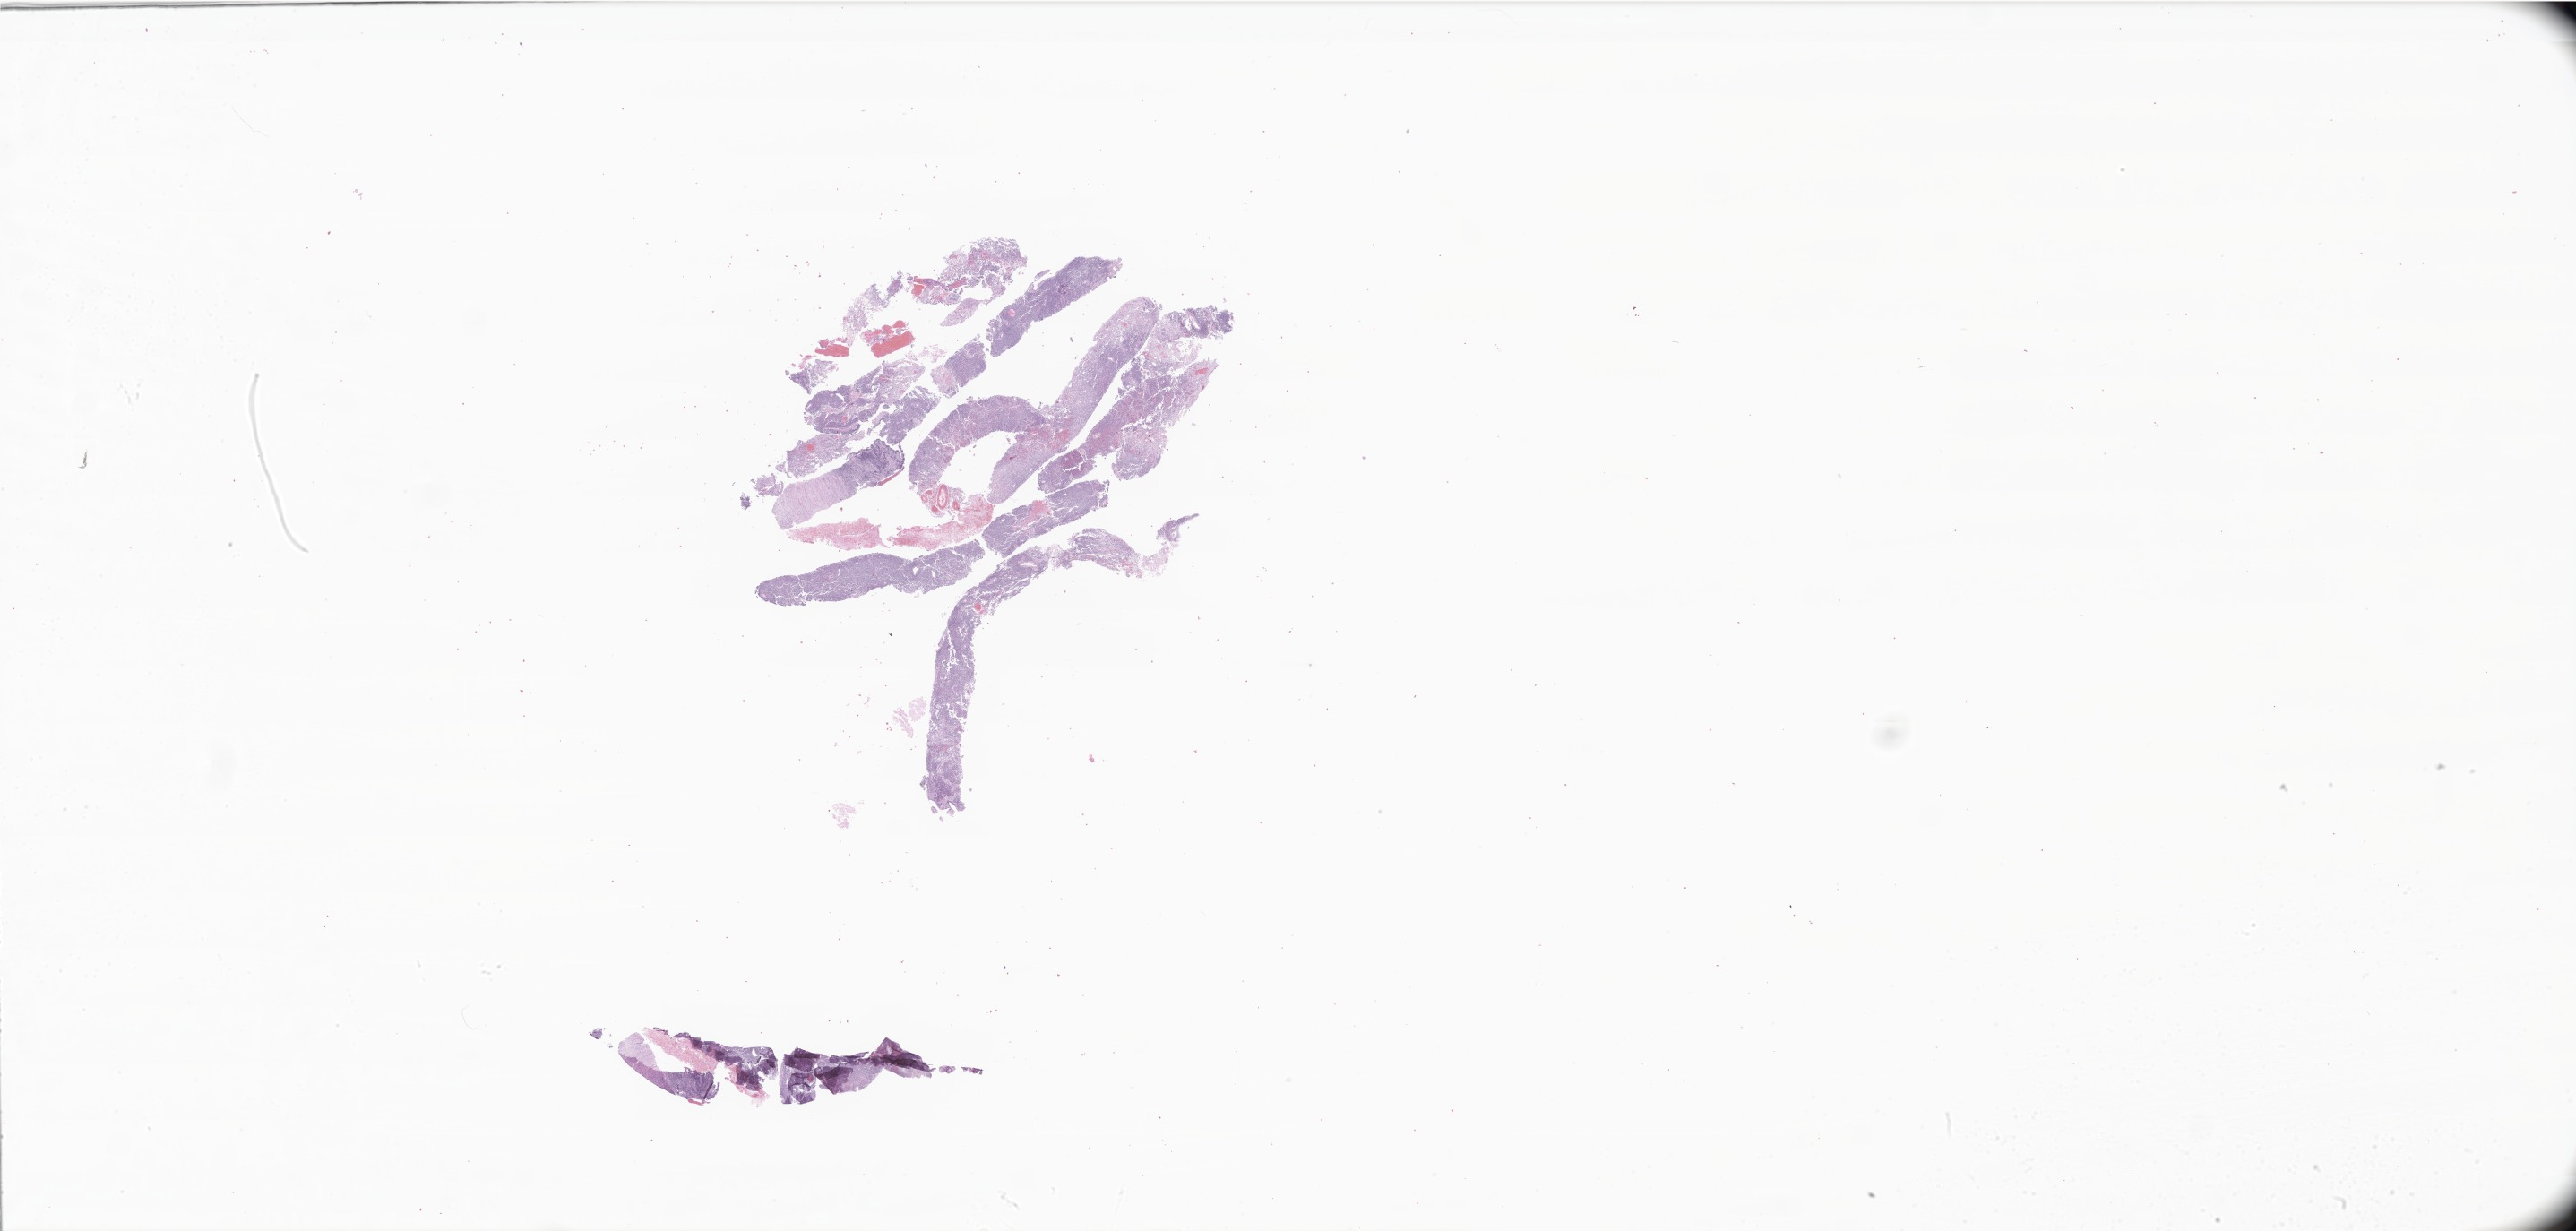
Digitized H&E-stained section of tumor tissue from the lower limb lymph node, whole scanned area (about 48.5 x 23.2 mm) shown as a low-resolution overview, formalin-fixed paraffin-embedded section. Patient male; age 277 months (23 years 1 month).
Diagnosis: Rhabdomyosarcoma, NOS. Tissue or organ of origin (case record): lymph nodes of inguinal region or leg.